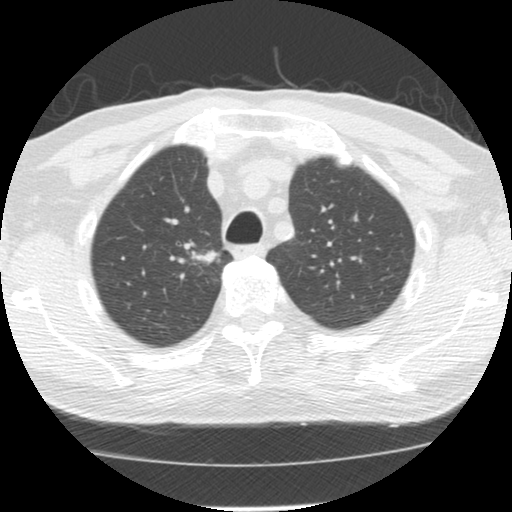
Chest CT (low-dose screening protocol), one axial image, baseline screening round, lung window (W 1500 / L -600 HU), slice 34 of 139 in the series, 512 × 512 image matrix. Male, age 64 years at enrolment.
Expert reader's lesion annotation, bounding box <172,234,224,277> (left, top, right, bottom; pixels). The exam's reader record, not a measurement of the box and not confirmed to be the same lesion: non-calcified nodule or mass ≥4 mm, right upper lobe, 20 × 13 mm, spiculated (stellate) margins, soft tissue attenuation. Official screen result: positive, change unspecified: nodule(s) >= 4 mm or enlarging nodule(s), mass(es), or other non-specific abnormalities suspicious for lung cancer. Participant outcome: lung cancer diagnosed 73 days after this screen — adenocarcinoma, NOS, right upper lobe, moderately differentiated (G2), stage IA (AJCC 6th edition), 17 mm at pathology.